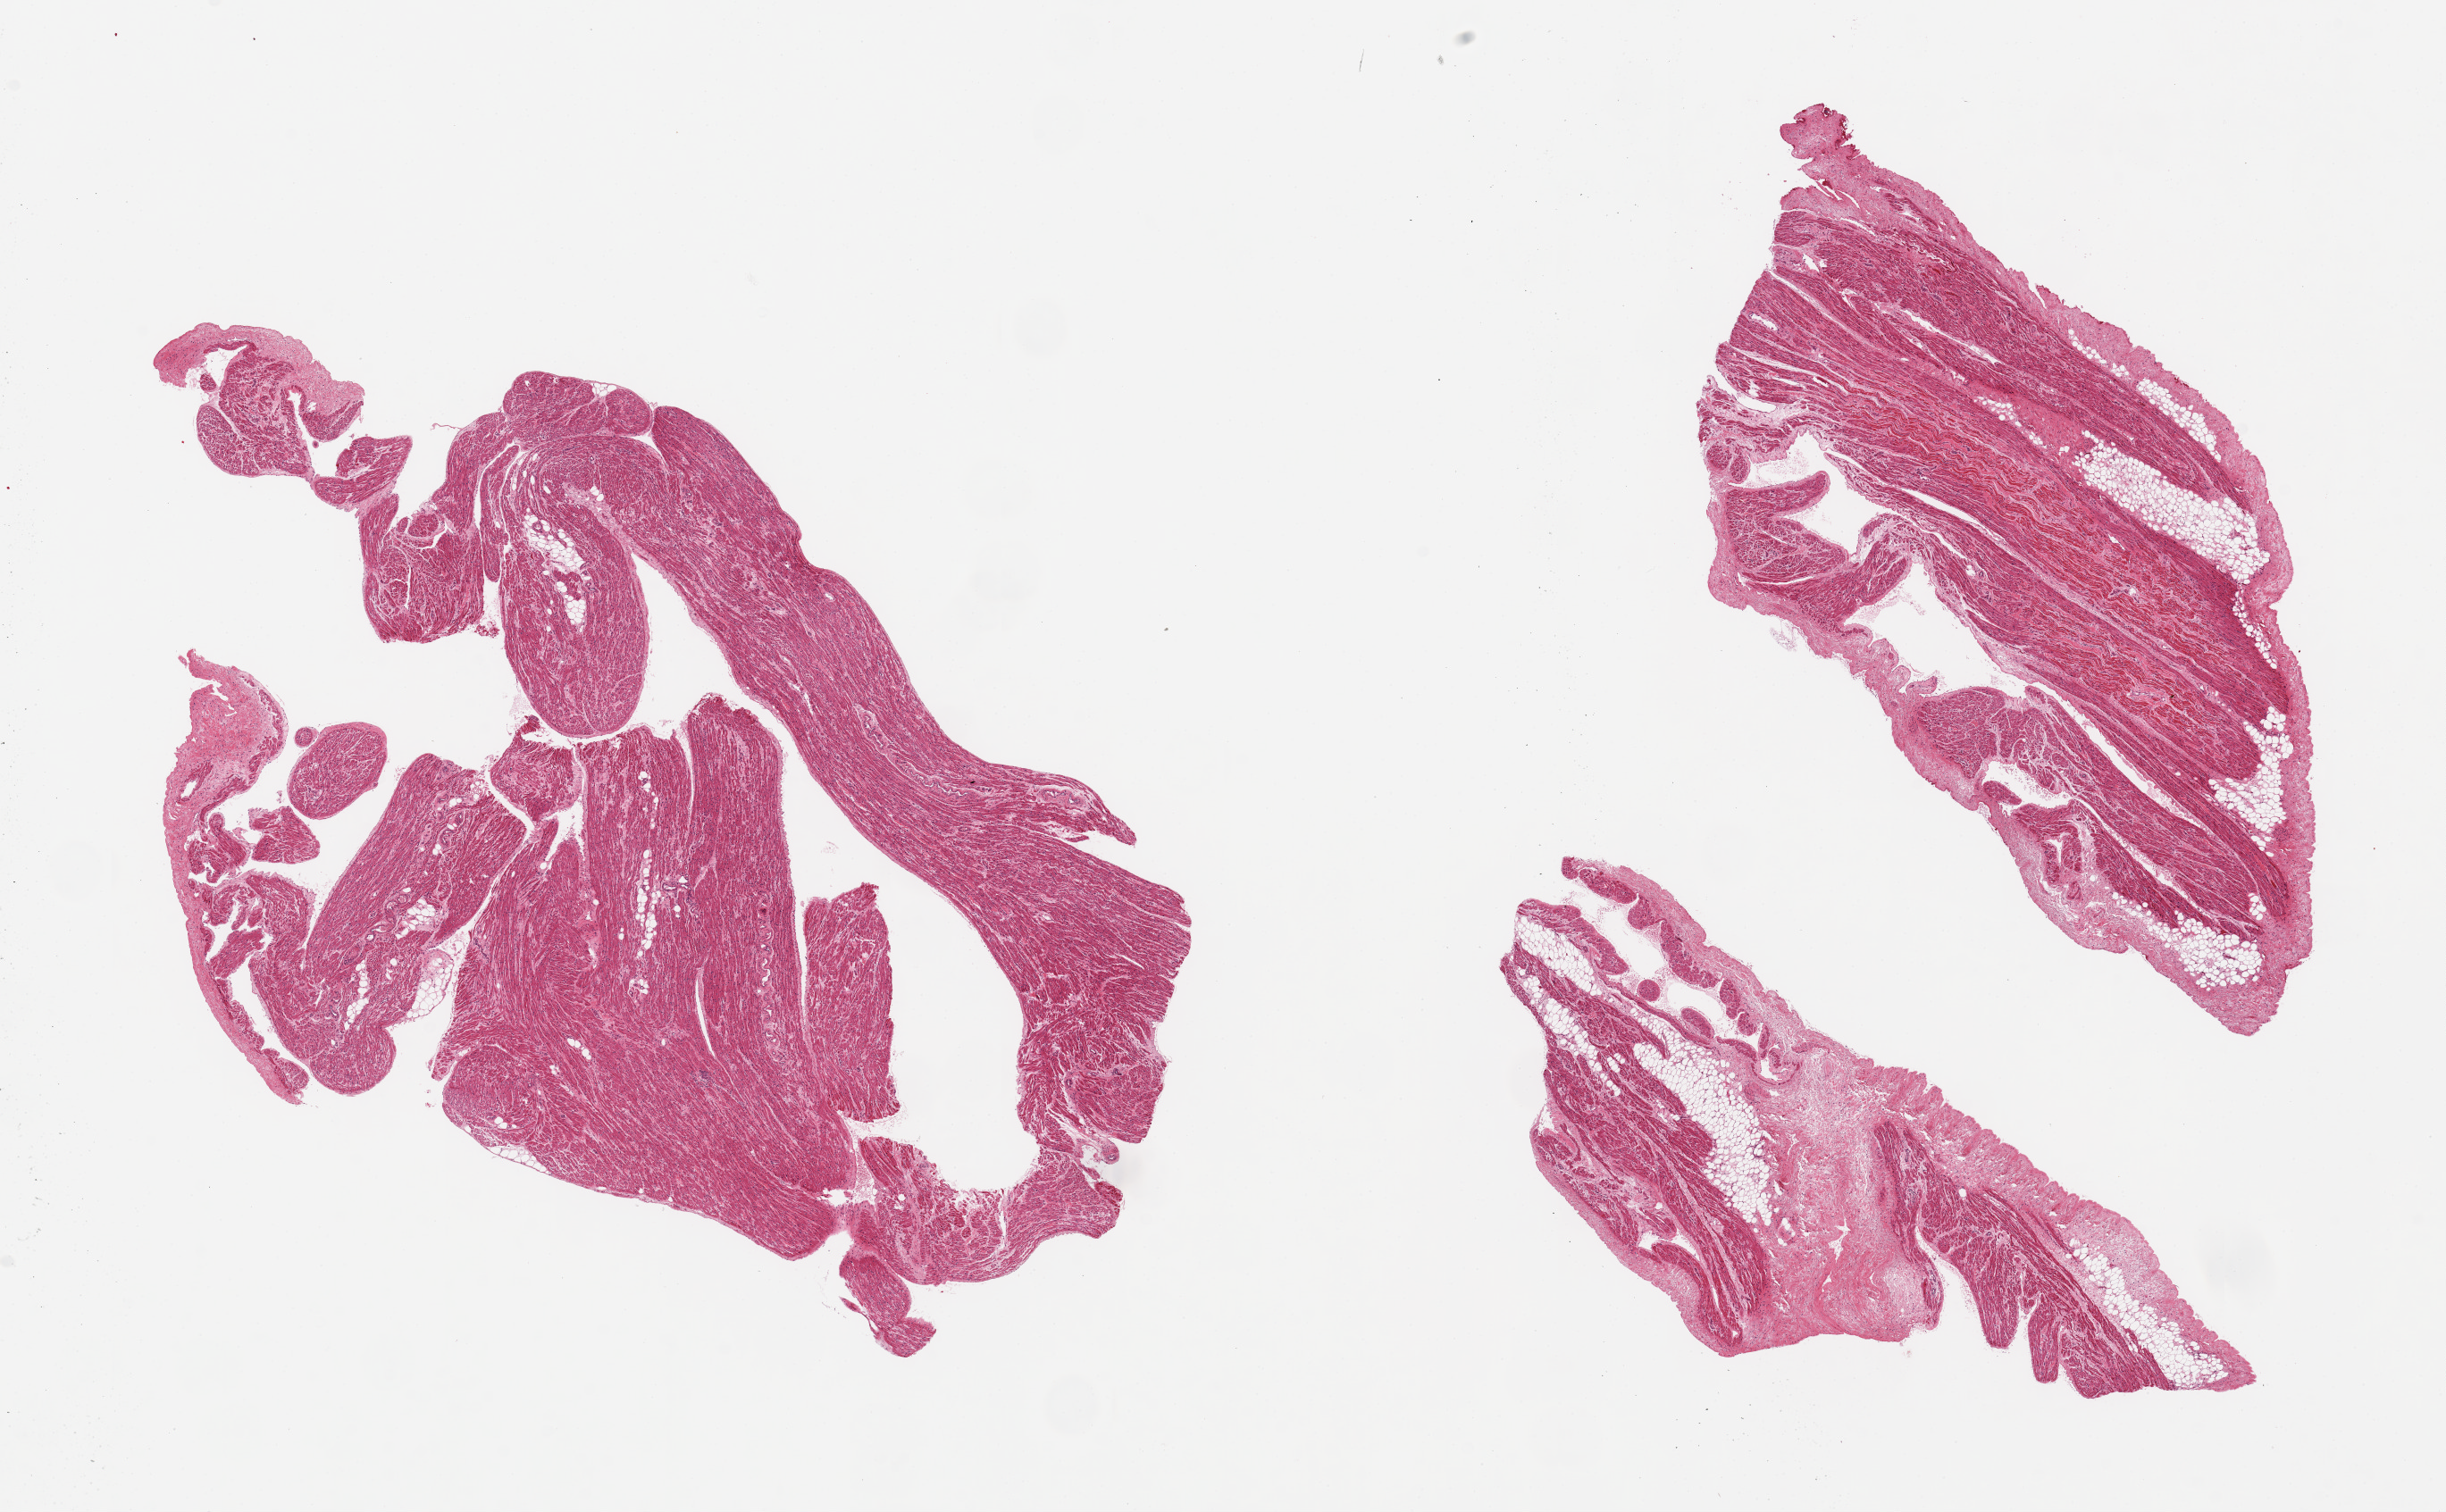
Whole-slide image, haematoxylin and eosin stain, shown as a low-resolution overview of the whole scanned area (about 21.7 x 13.4 mm); PAXgene-fixed, paraffin-embedded tissue; sampled site (target tissue): auricular appendage; donor tissue sample.
Reviewer comment on this tissue sample: 3 pieces, no abnormalities.